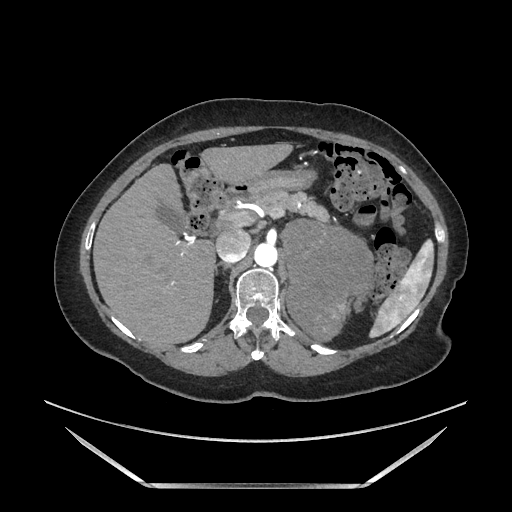
Contrast-enhanced abdominal CT, one axial slice; slice 114 of 205 in the series (ordered by position); soft-tissue window (W 400 / L 40 HU); 1.25 mm slice thickness; 512 × 512 image matrix, field of view 440 × 440 mm. Female patient. Case-level facts recorded for this patient, not image findings: diagnosis: adrenocortical carcinoma; tumour side: left adrenal; tumour size at pathology: 12.5 cm; Ki-67 index: 39 %; stage (as recorded): 3.
Structures marked on this image (semi-automatic segmentation, software-assisted and operator-edited):
- mass: bounding box <287,222,374,336> (left, top, right, bottom; pixels)